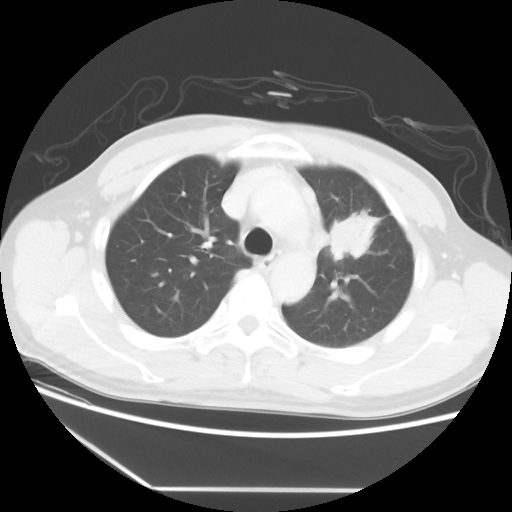
Chest CT, one axial slice; position 40 of 56 along the scan axis; reconstruction kernel STANDARD; 120 kVp; lung window (W 1500 / L -600 HU); 5 mm slice thickness; 512 × 512 image matrix, field of view 373 × 373 mm. Patient: male, 53 years. Case-level facts recorded for this patient, not image findings: clinical TNM (as recorded): T2a N1 M1b.
Structures marked on this image (rectangle marked by the reading radiologist):
- lung tumour (recorded histology: adenocarcinoma): box from (x=328, y=213) to (x=380, y=262) px